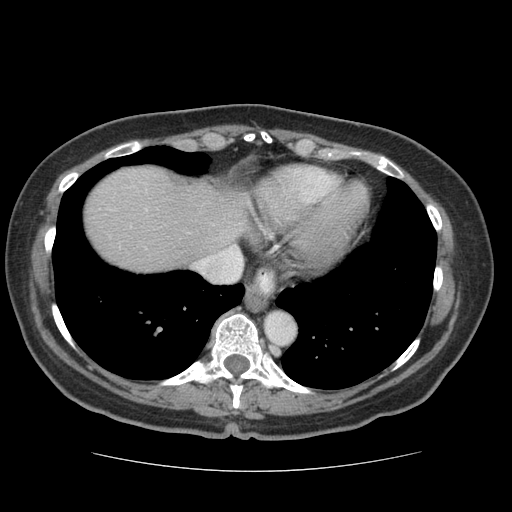
Contrast-enhanced abdominal CT (liver protocol), one axial slice. Position 65 of 75 along the scan axis. Reconstruction kernel STANDARD. 140 kVp. Soft-tissue window (W 400 / L 40 HU). 2.5 mm slice thickness. 512 × 512 image matrix, field of view 360 × 360 mm. Case-level facts recorded for this patient, not image findings: diagnosis: hepatocellular carcinoma (patient treated with transarterial chemoembolisation; whether this scan precedes or follows treatment is not stated here); TNM stage (as recorded): Stage-I; Child-Pugh class: A.
Structures marked on this image (semi-automatically segmented with operator editing):
- liver parenchyma outside the tumour (the mass and vessels are separate outlines, so this box may not span the whole liver): bounding box (x1, y1, x2, y2) in pixels: (84, 166, 251, 272)